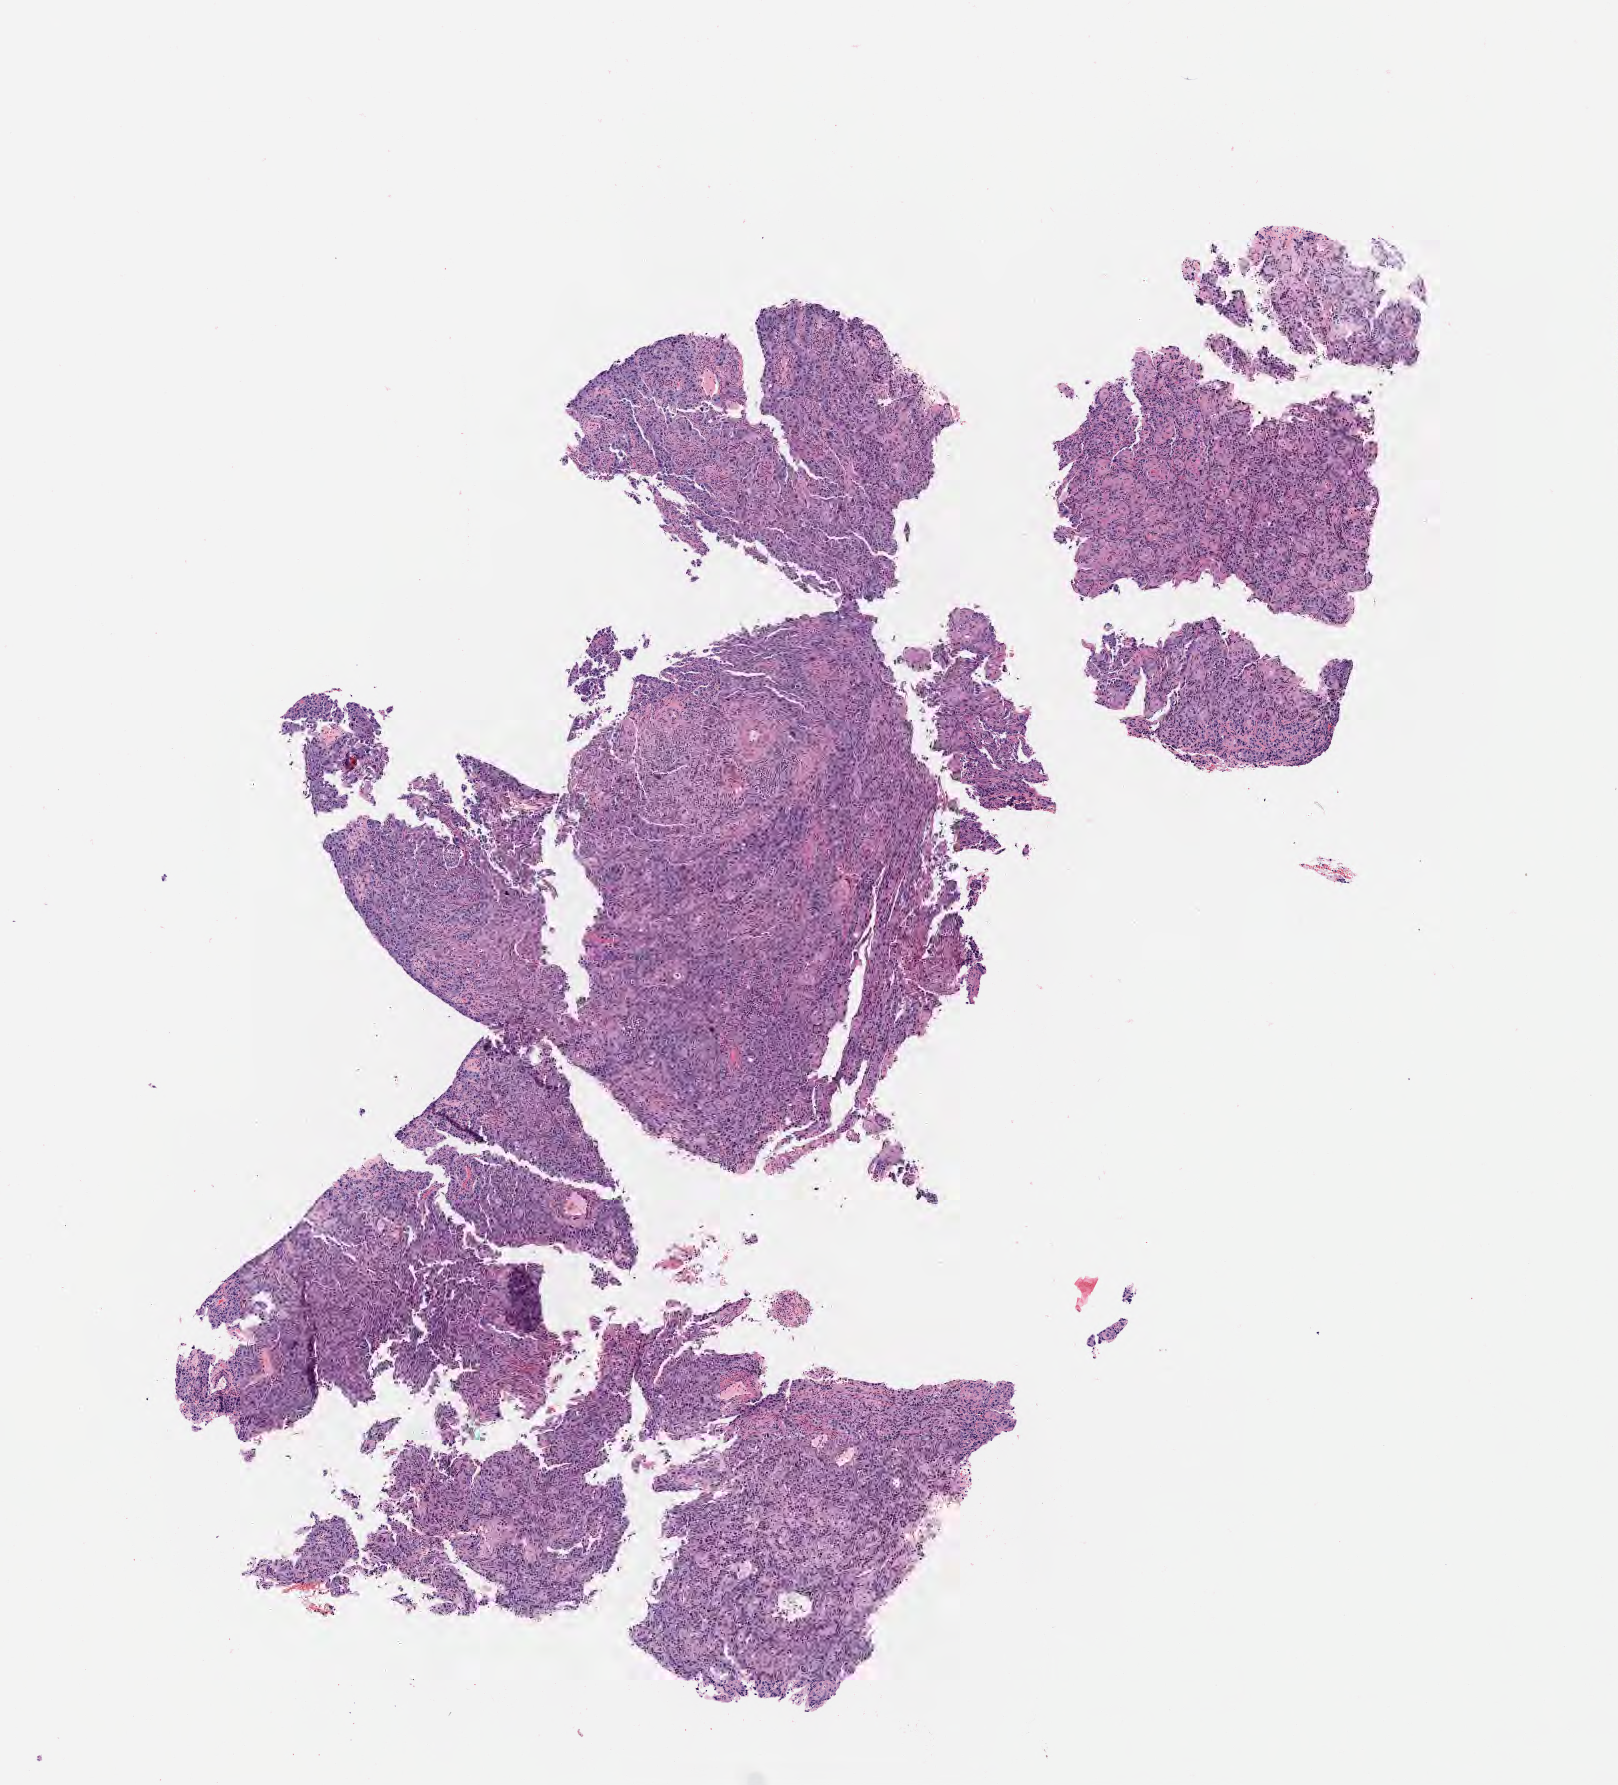
Digitized H&E-stained section — low-resolution overview of the scanned area, about 6.5 x 7.2 mm, specimen: tumor tissue, site: cervix. Patient female; 50 years old.
Histologic diagnosis: Squamous cell carcinoma, keratinizing, NOS.